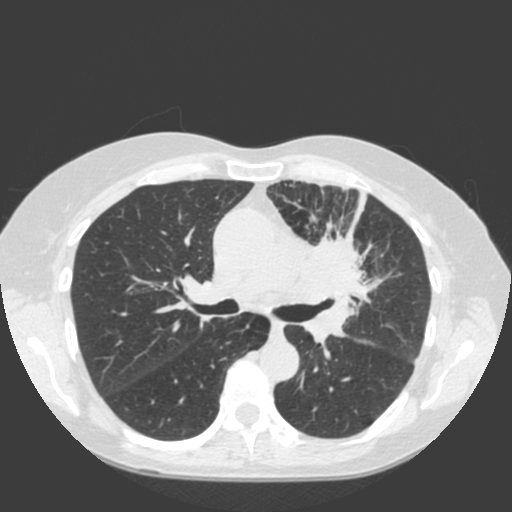
Low-dose screening chest CT, one axial slice; slice 117 of 184 in the series (ordered by position); lung window (W 1500 / L -600 HU); 512 × 512 image matrix, field of view 350 × 350 mm.
Annotated regions visible in this slice (manually delineated by an expert):
- lesion 1 (tumor, hilum of left lung): box from (x=298, y=231) to (x=378, y=351) px